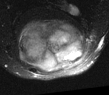
MRI of an extremity soft-tissue mass, one axial slice. Position 28 of 52 along the scan axis. T2-weighted fat-saturated. MR volume resampled by the dataset authors to the PET/CT grid (not the native acquisition matrix). 3.27 mm slice thickness. 109 × 95 image matrix, field of view 106 × 93 mm. Male patient. From the clinical record (not read from this slice): histological type: synovial sarcoma; site of the primary tumour: left poplietal fossa.
Structures marked on this image (expert contour drawn on MRI and transferred to this co-registered scan by the dataset authors):
- gross tumour volume (mass): box from (x=15, y=17) to (x=86, y=73) px